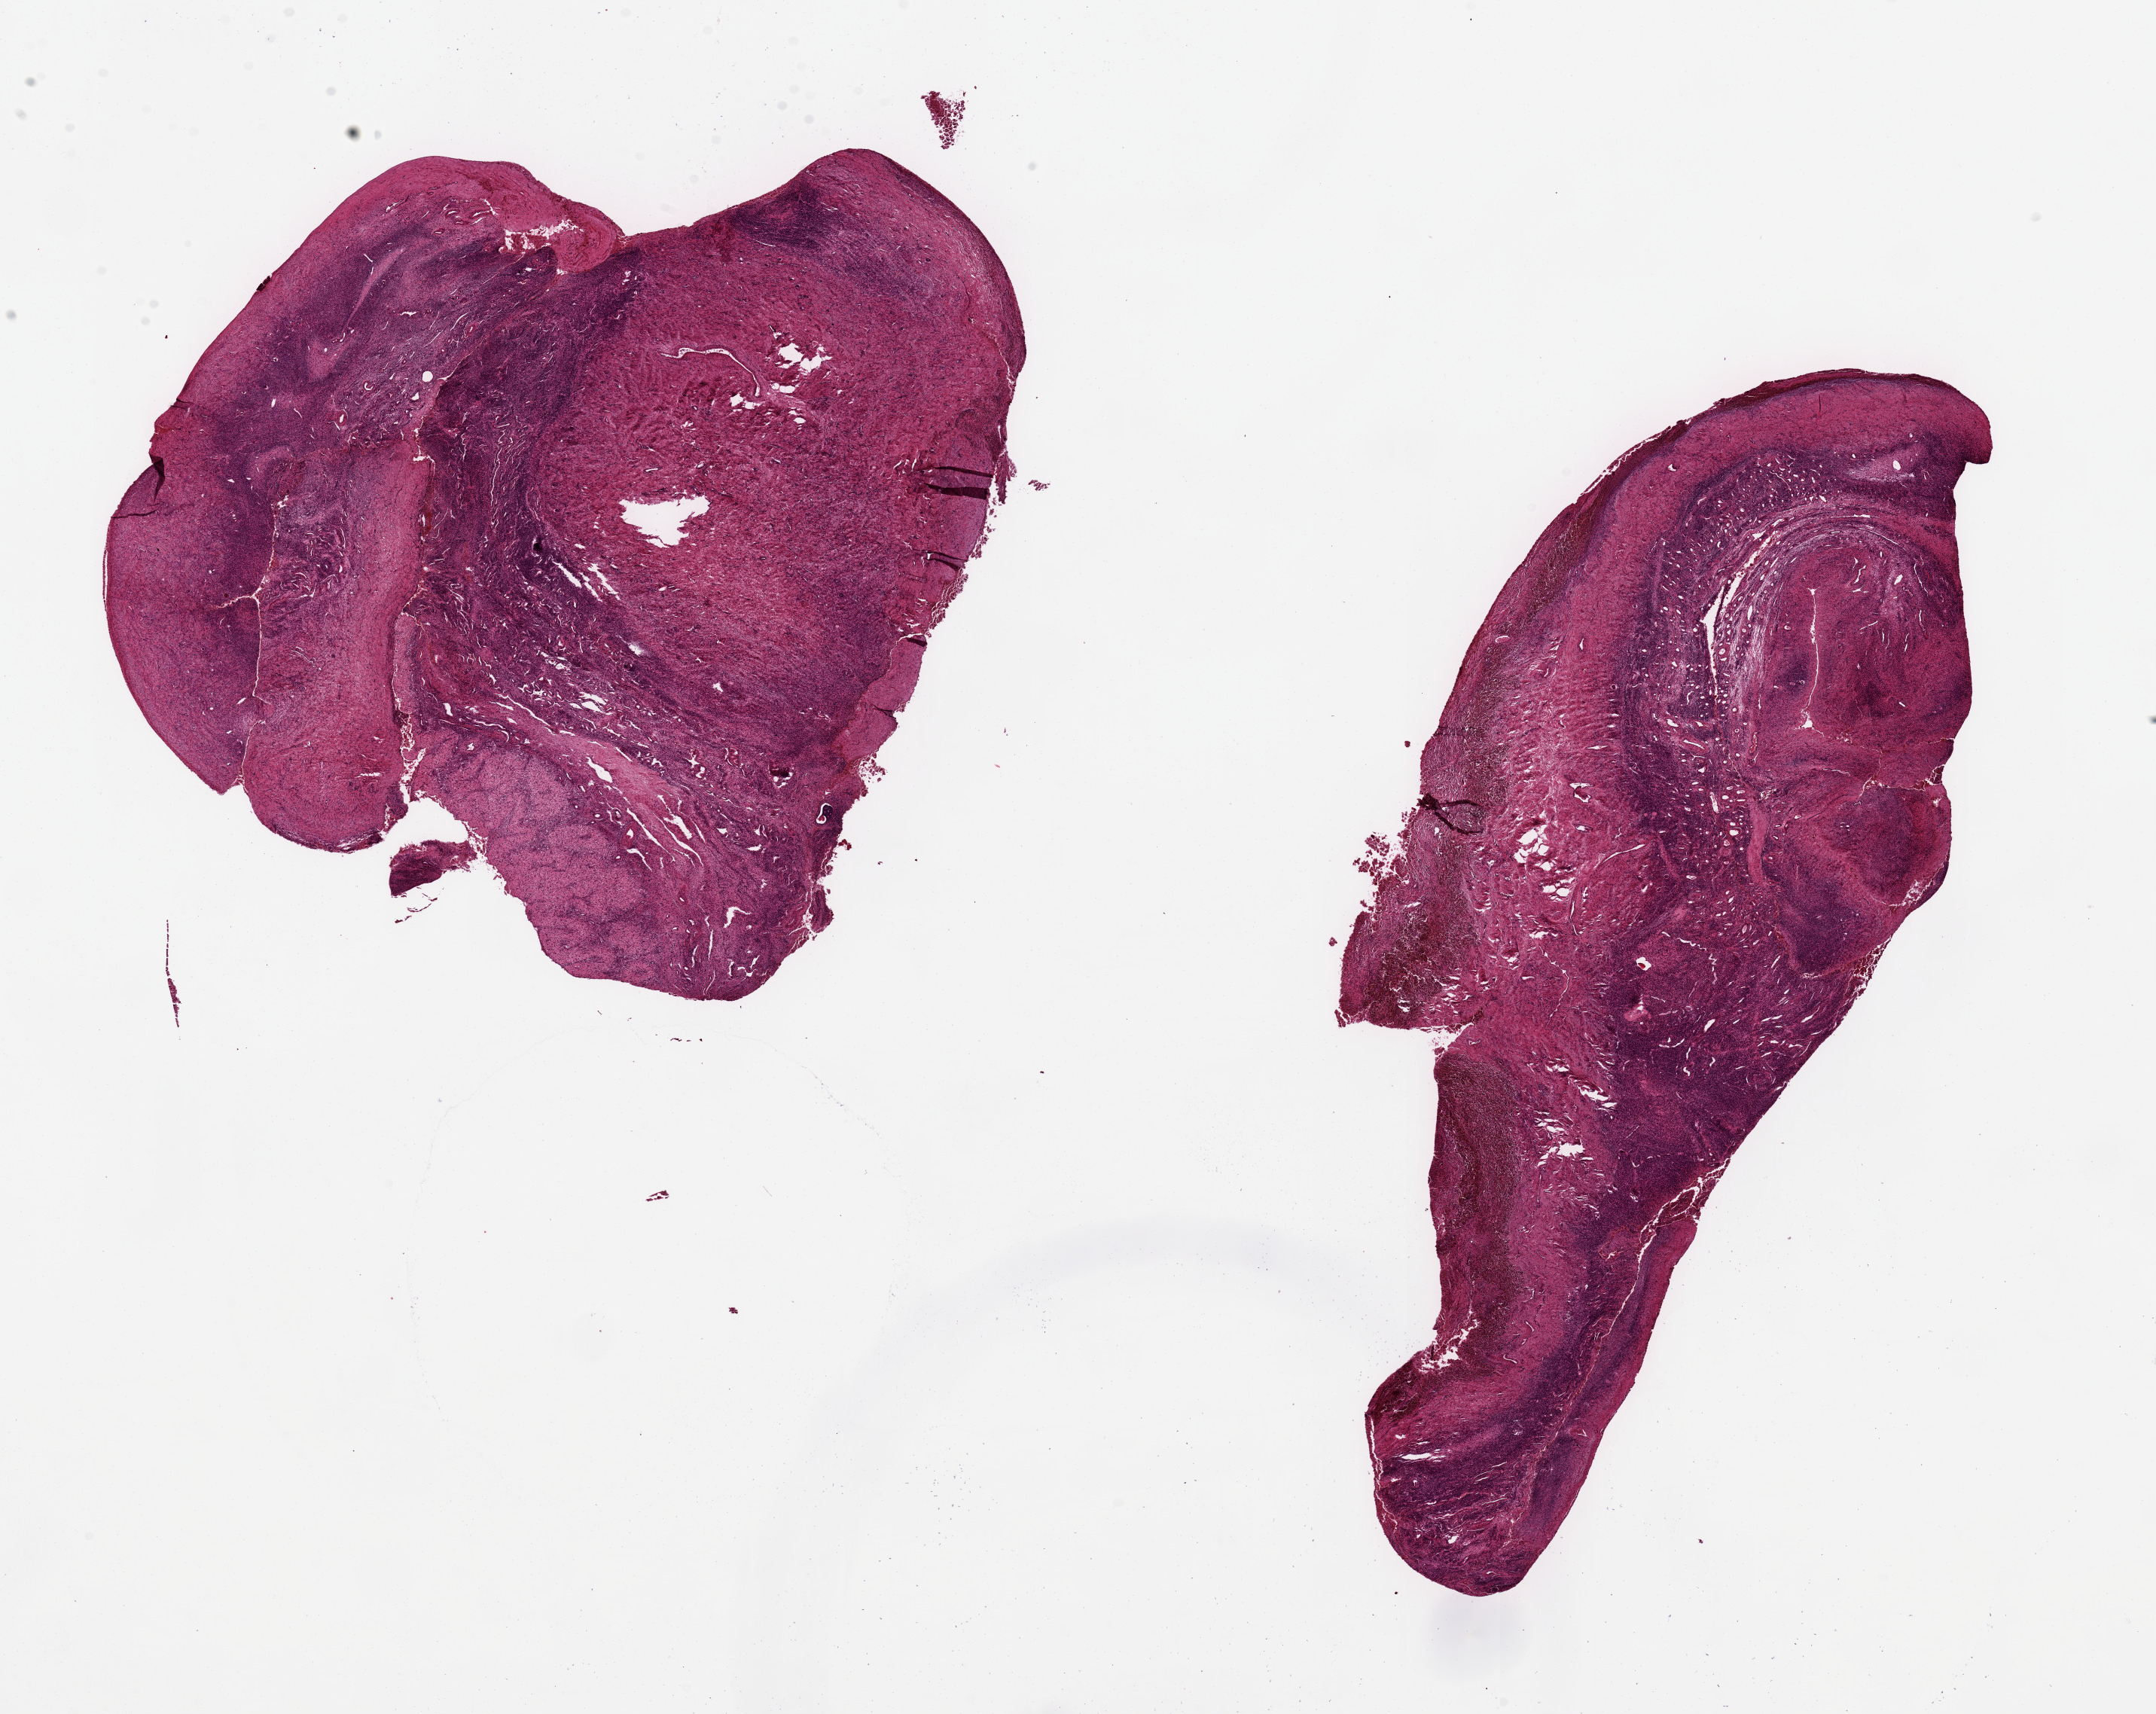
Hematoxylin and eosin (H&E) whole-slide image, shown as a low-resolution overview of the whole scanned area (about 22.6 x 18.0 mm, acquisition: 20x scan); PAXgene-fixed paraffin-embedded (PFPE) section; section of ovary (target tissue); donor tissue sample. Donor sex: female.
Pathologist's review note for this sample: 2 pieces, ~8x8 & 13x5mm; a few primordial follicles; probable old endometriosis.